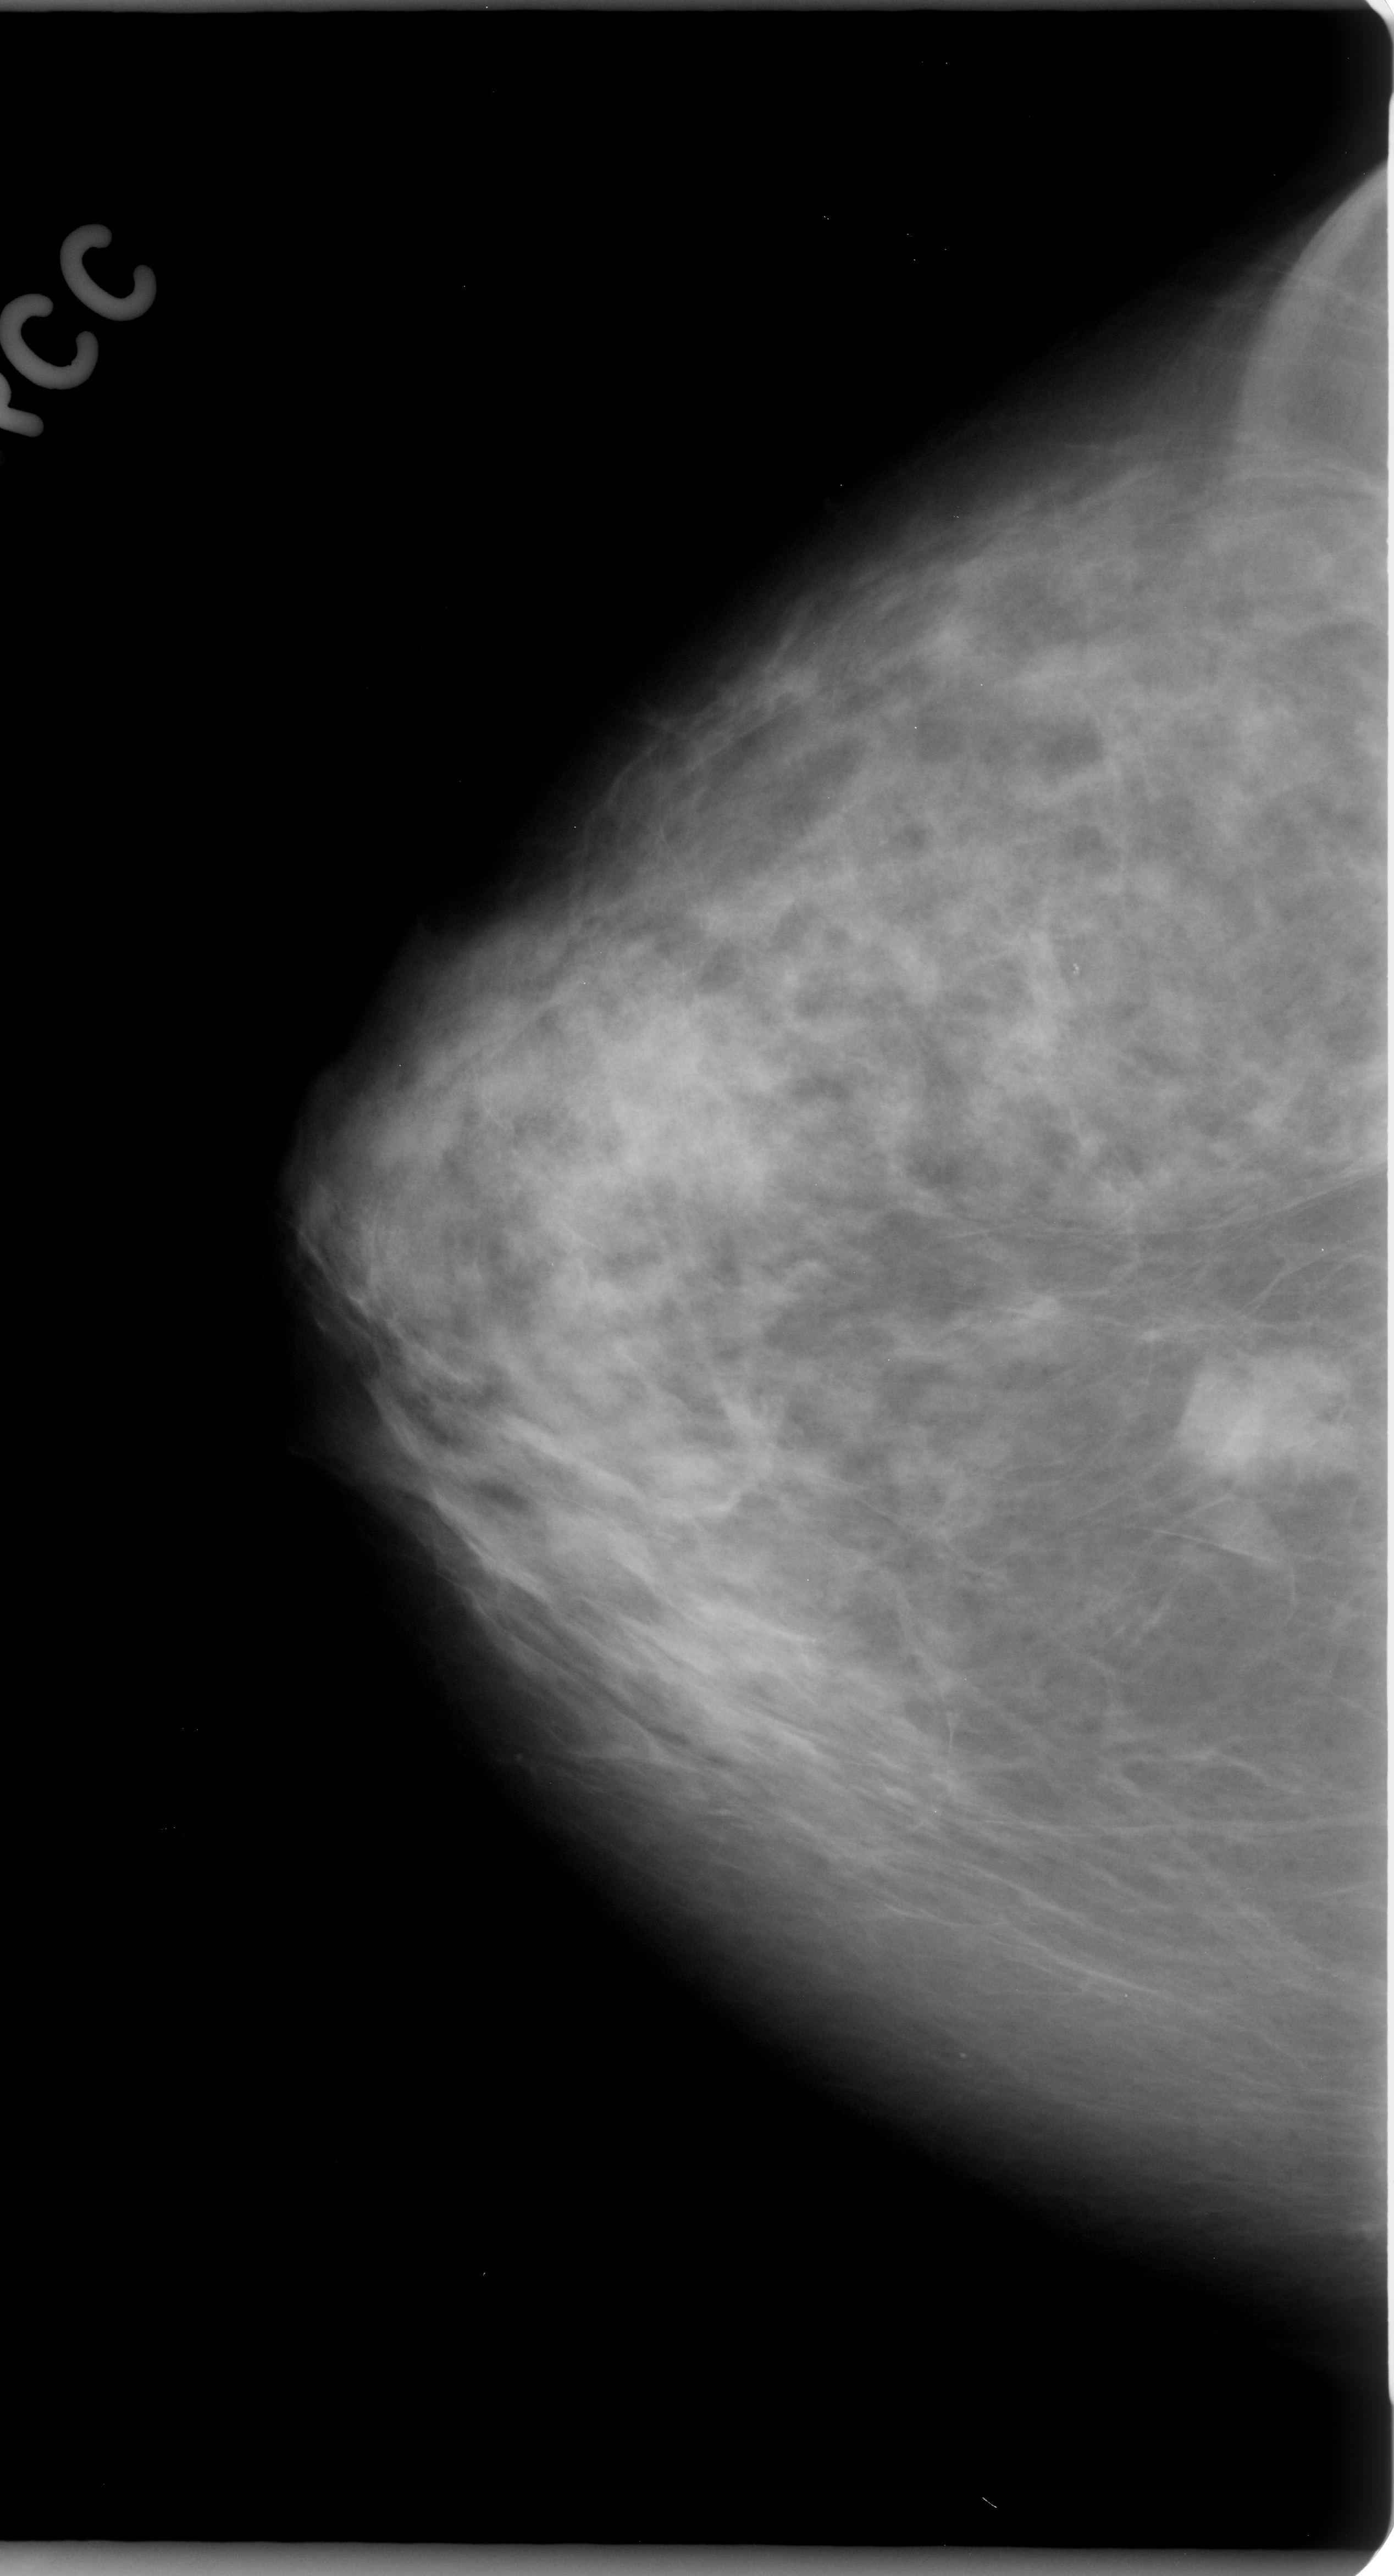
Scanned film-screen mammogram; right breast; CC view; breast composition: scattered fibroglandular densities (BI-RADS density category 2 of 4).
Mass, shape irregular, margins spiculated; BI-RADS assessment category 5; subtlety rating 5 on a 1 (subtle) to 5 (obvious) scale; pathology result (as recorded, not read from the image): malignant.